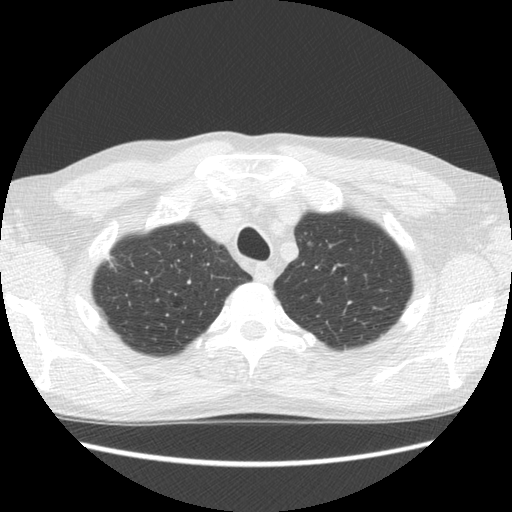
Low-dose screening chest CT, one axial slice; slice 104 of 125 in the series (ordered by position); lung window (W 1500 / L -600 HU); 512 × 512 image matrix.
Structures marked on this image (outlined manually by an expert reader):
- lesion 1 (tumor, upper lobe of right lung): bounding box [x1, y1, x2, y2] px = [104, 253, 114, 265]